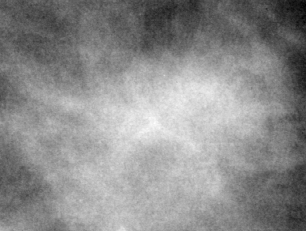
Cropped region of a digitized screen-film mammogram centred on a radiologist-marked abnormality; left breast; CC view; BI-RADS breast density category 3 (scale 1–4).
Finding: mass, shape lobulated, margins circumscribed / ill defined; BI-RADS assessment category 3; pathology result (as recorded, not read from the image): malignant.